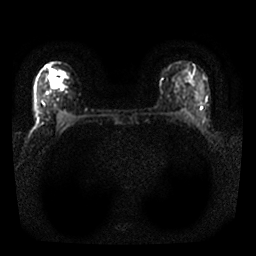
Breast MRI, one axial slice. Slice 20 of 25 in the series (ordered by position). Diffusion-weighted series; image 2 of 4 stored at this slice position (different b-values; order by instance number). 1.5 T. 256 × 256 image matrix, field of view 310 × 310 mm. Female patient.
Structures marked on this image (manually delineated by an expert):
- tumour on diffusion-weighted imaging: bounding box <48,70,60,83> (left, top, right, bottom; pixels)